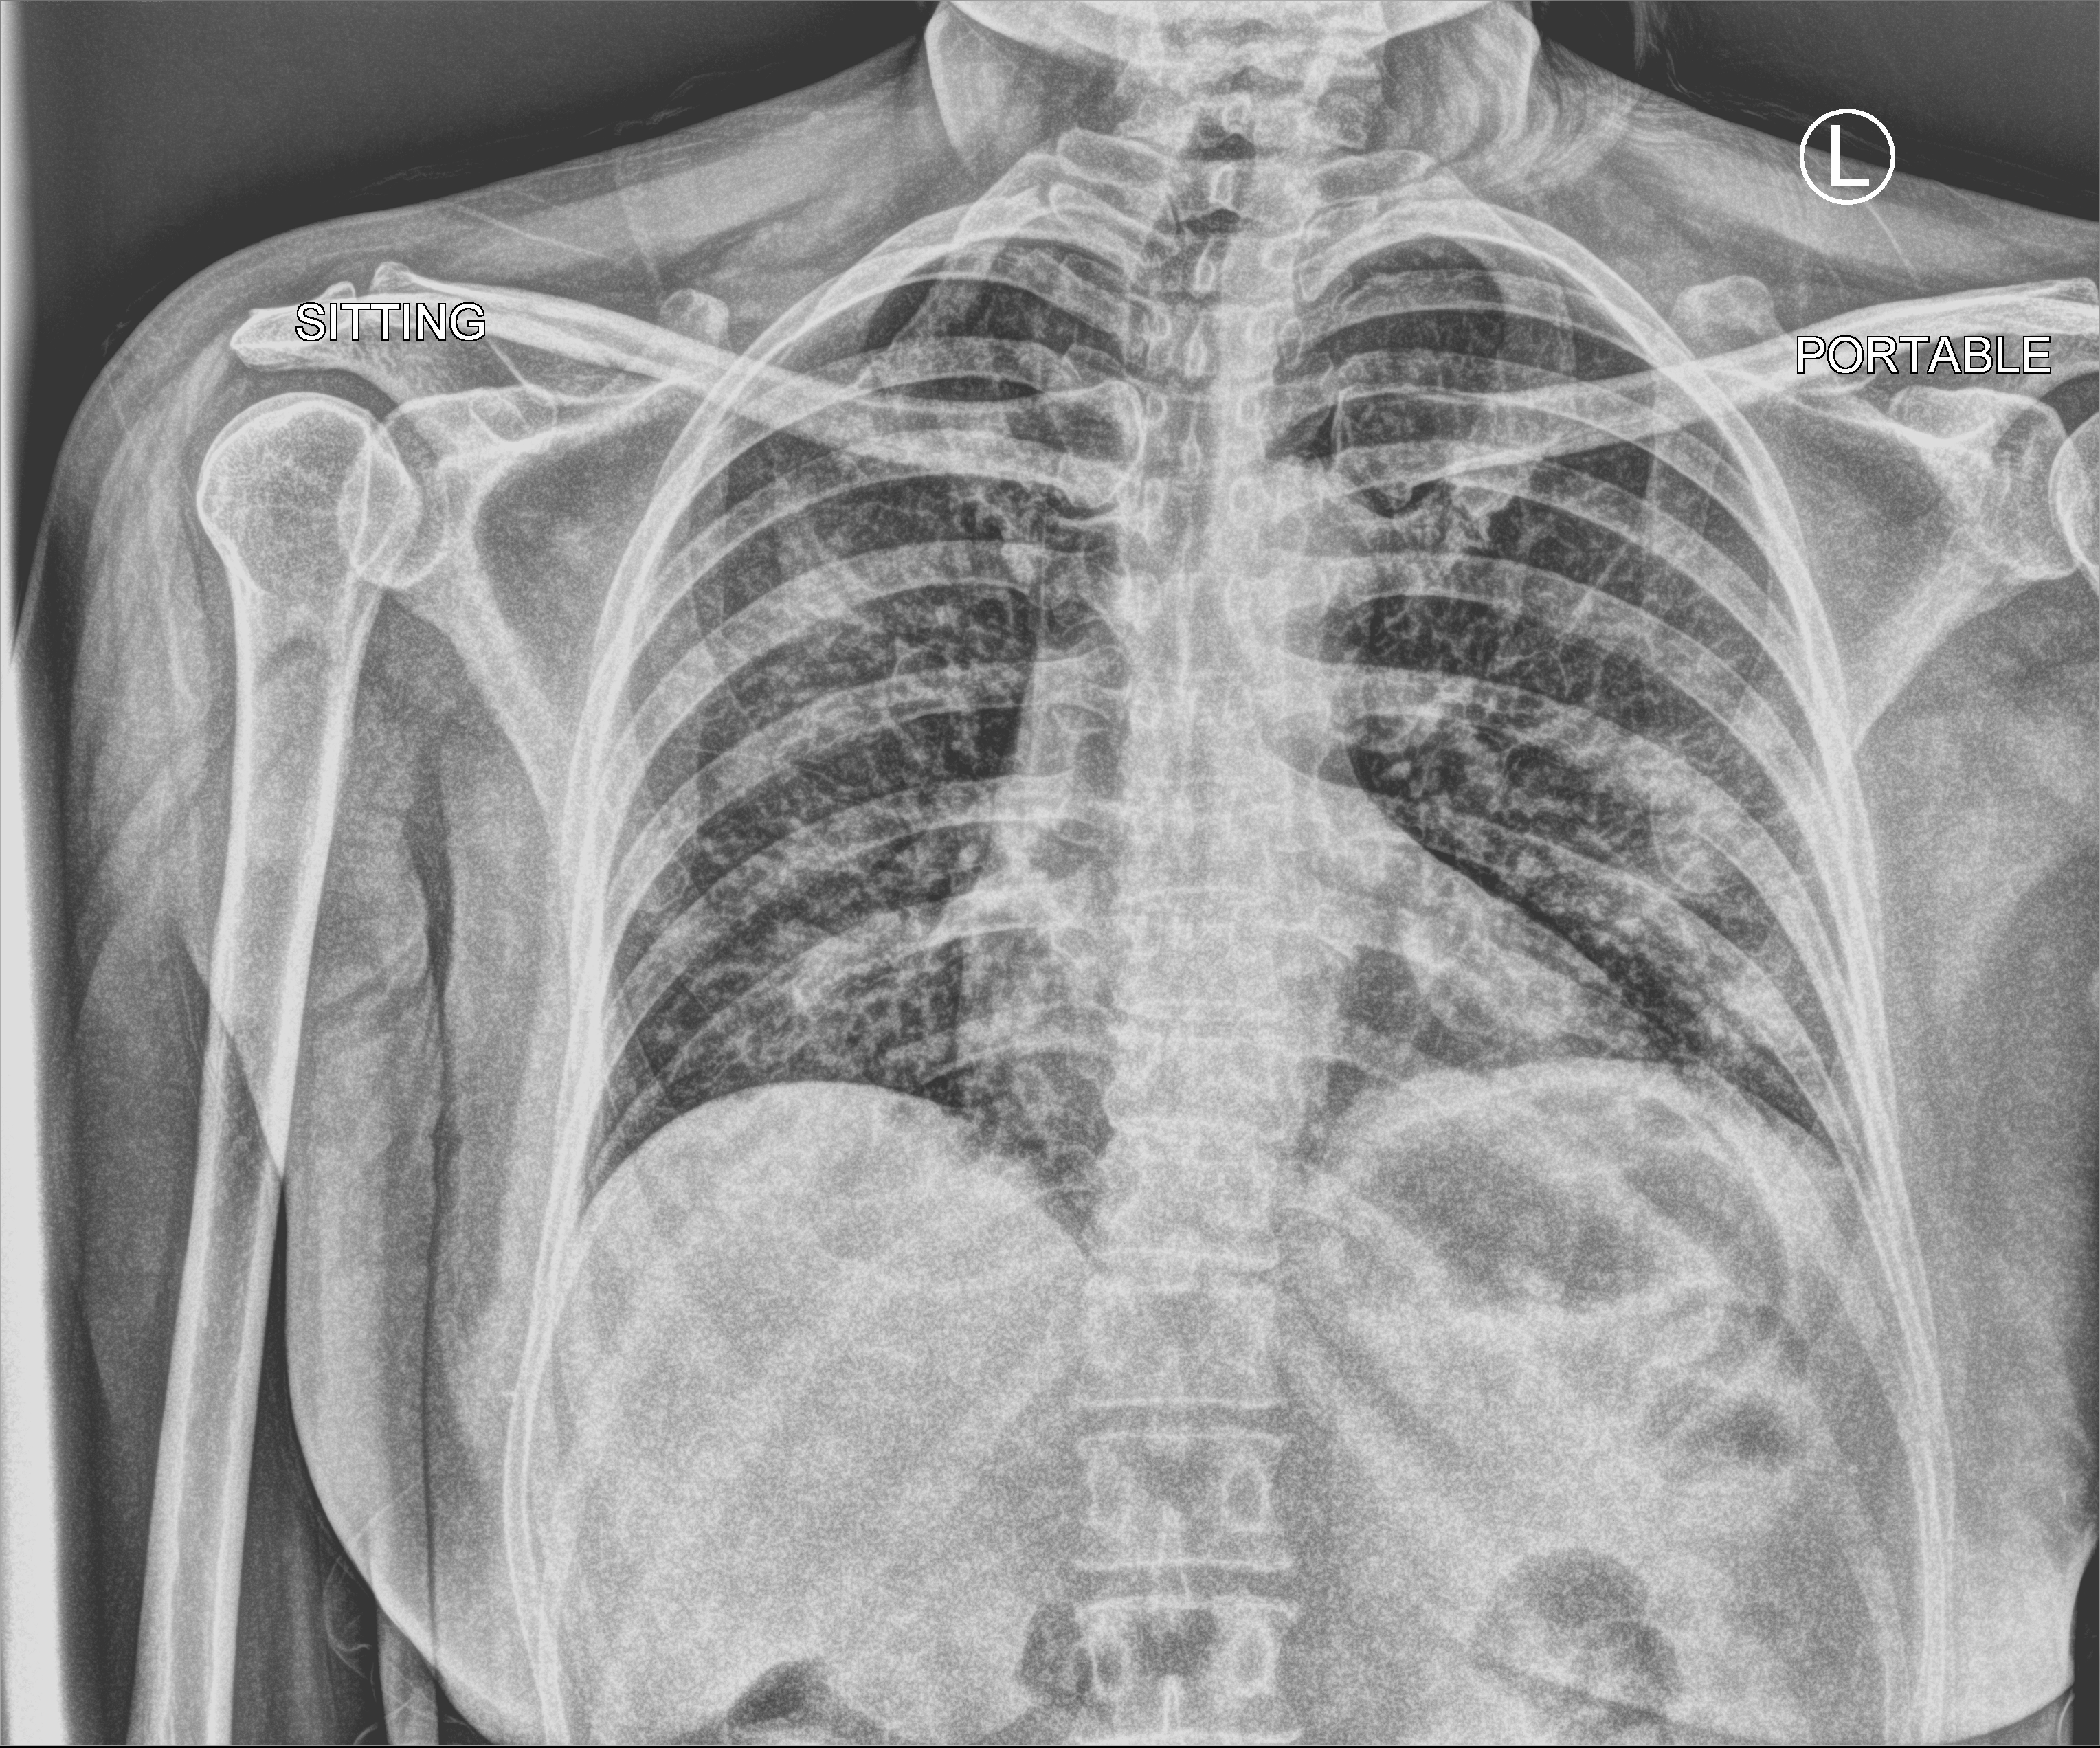
Bedside chest radiograph (computed radiography); anteroposterior (AP) projection. Female patient hospitalised with COVID-19, age 18–59 years.
Admission-level facts for this patient (not findings on this image; timing relative to this image not recorded):
- admitted to intensive care during this hospital stay: no